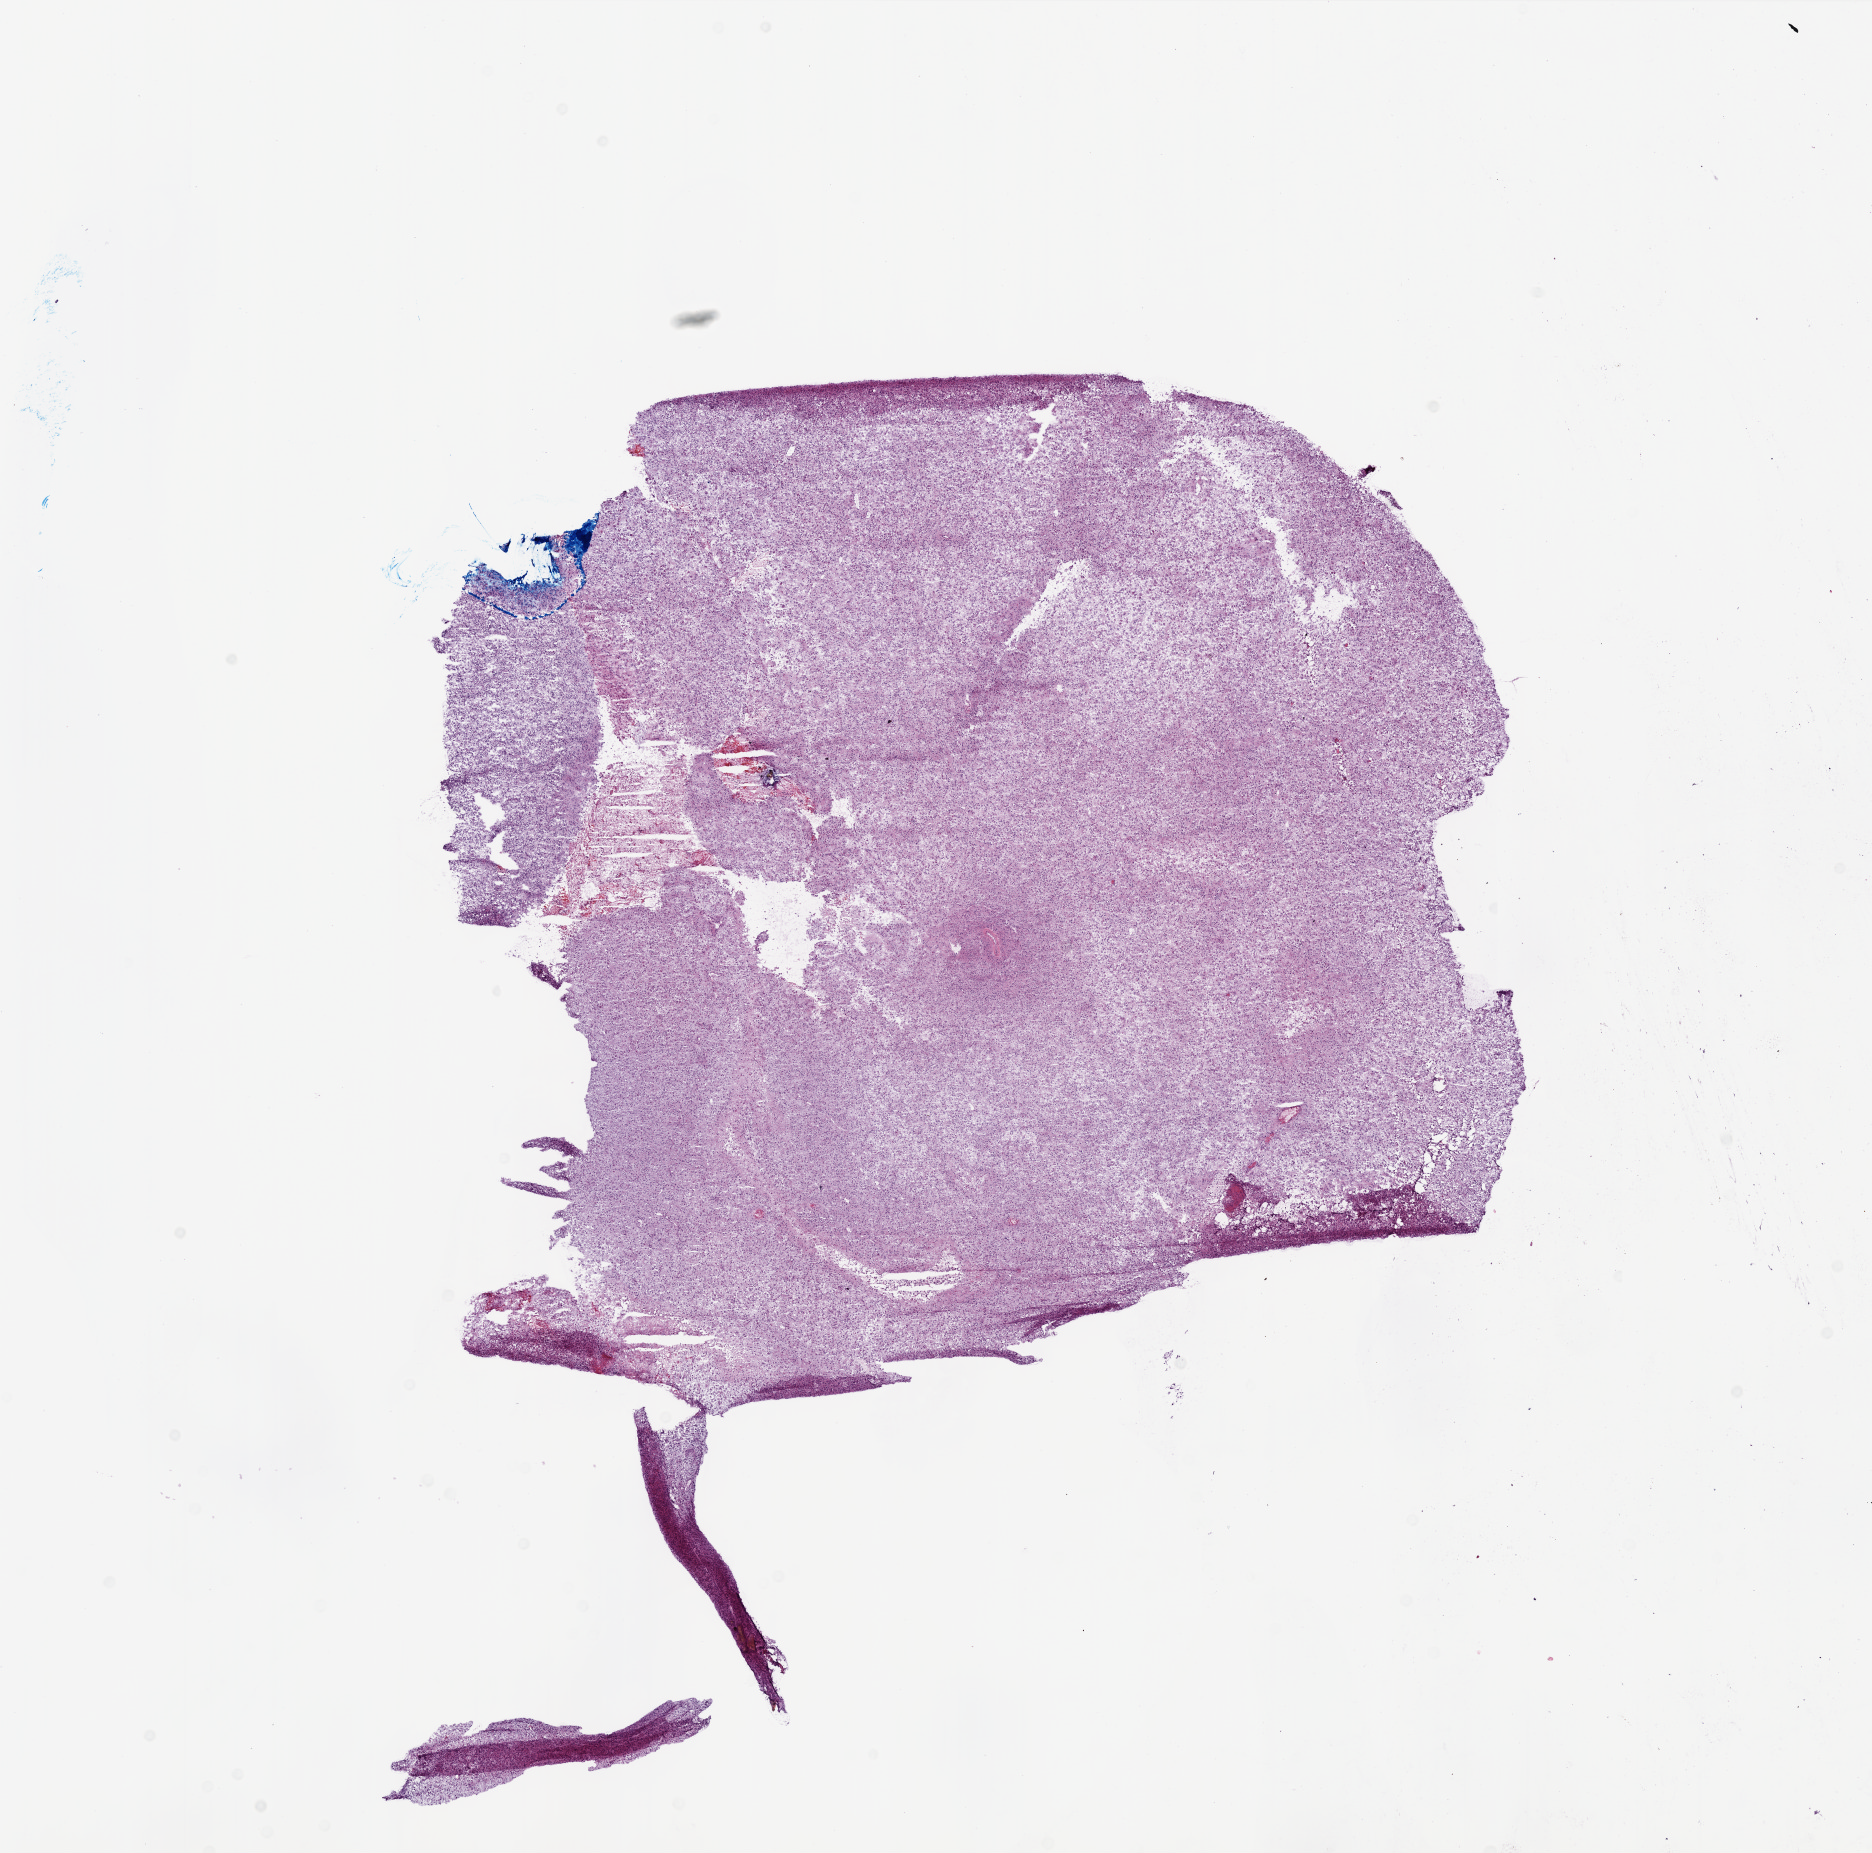
Digitized H&E-stained tissue section (whole slide), shown as a low-resolution overview of the whole scanned area (about 15.0 x 14.8 mm, slide scanned at 20x); frozen section; sample: primary tumour, brain. Male patient; age at initial diagnosis 52 years. Slide review estimates, as recorded: tumour cells 95%, tumour nuclei 95%, normal cells 0%, stromal cells 0%, necrosis 5%.
Histologic diagnosis: Glioblastoma.